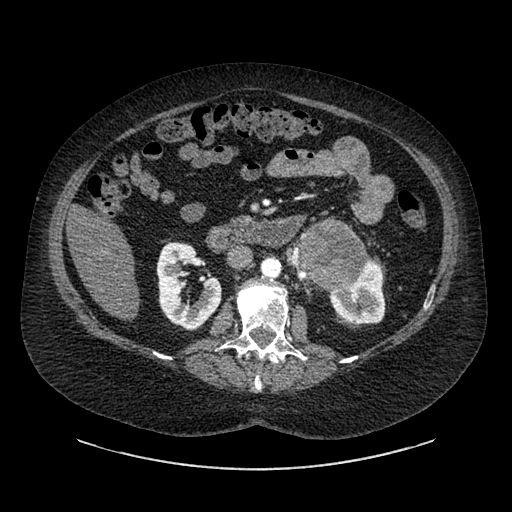
Contrast-enhanced abdominal CT, one axial slice; position 509 of 769 along the scan axis; intravenous contrast given; soft-tissue window (W 400 / L 40 HU); 0.62 mm slice thickness; 512 × 512 image matrix. Female patient, age 61 years. From the clinical record (not read from this slice): diagnosis: adrenocortical carcinoma; tumour side: left adrenal; tumour size at pathology: 13 cm; Ki-67 index: 79 %; stage (as recorded): 2.
Annotated regions visible in this slice (semi-automatic segmentation, software-assisted and operator-edited):
- mass: bounding box [x1, y1, x2, y2] px = [297, 224, 364, 288]